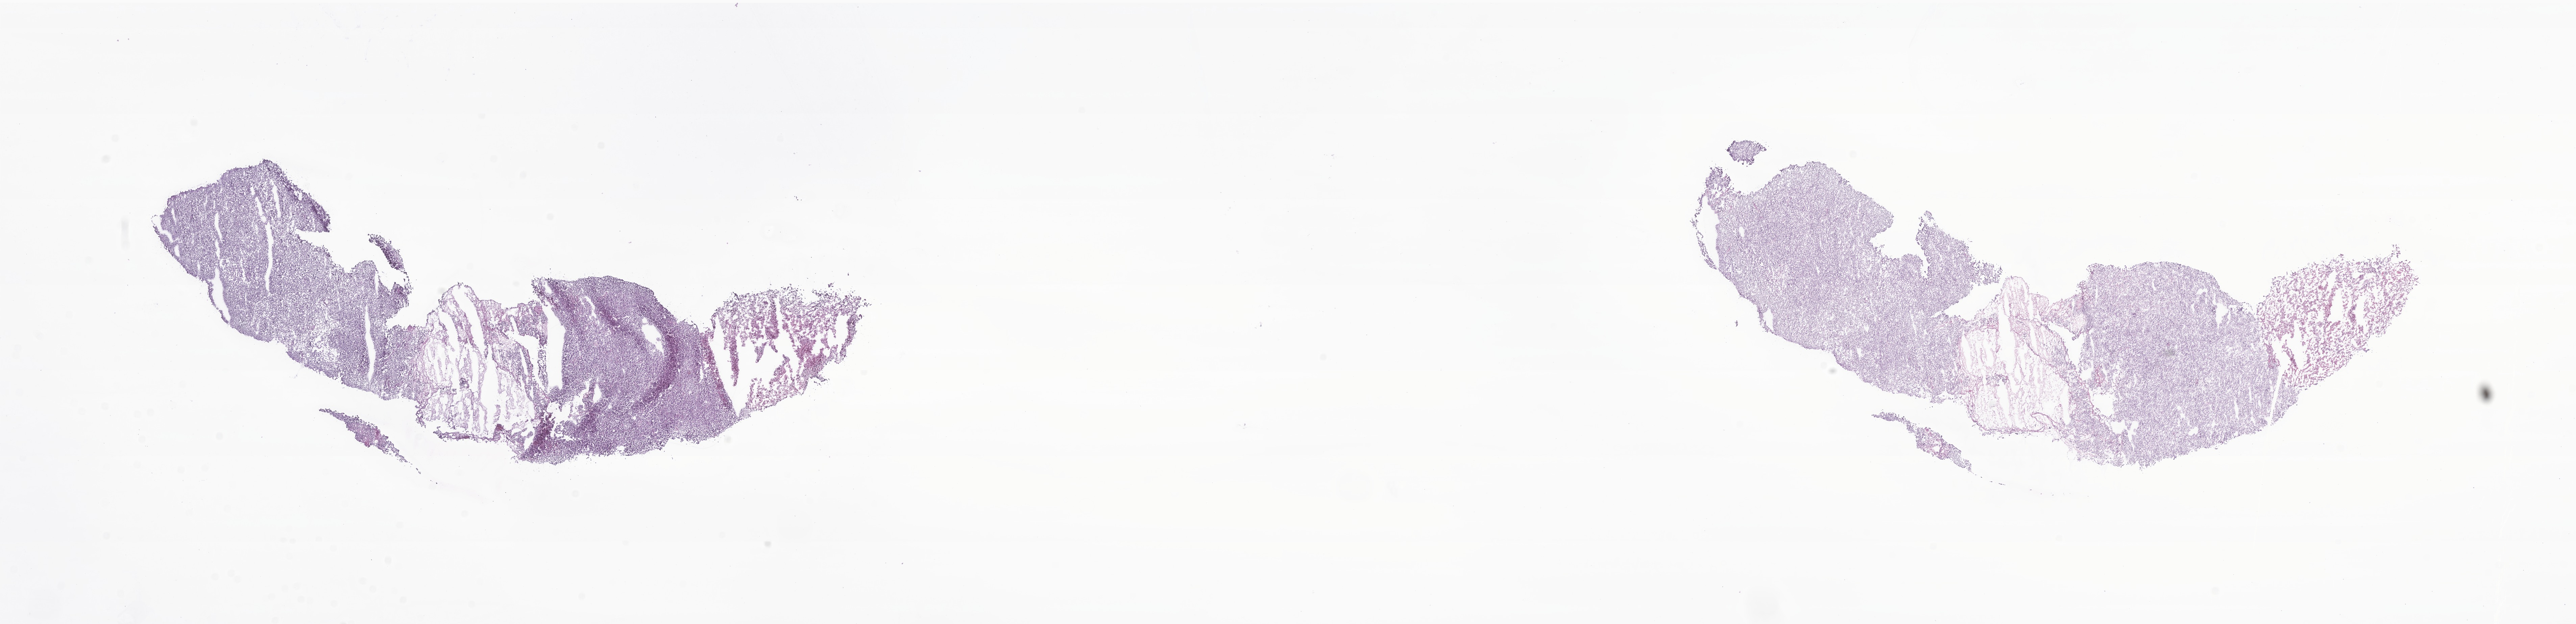
Digitized hematoxylin and eosin (H&E)-stained section of tumor tissue from the frontal lobe, shown as a low-resolution overview of the whole scanned area (about 32.1 x 7.8 mm). Frozen section. Female patient, age 214 months (17 years 10 months).
Diagnosis: Neoplasm, uncertain whether benign or malignant.